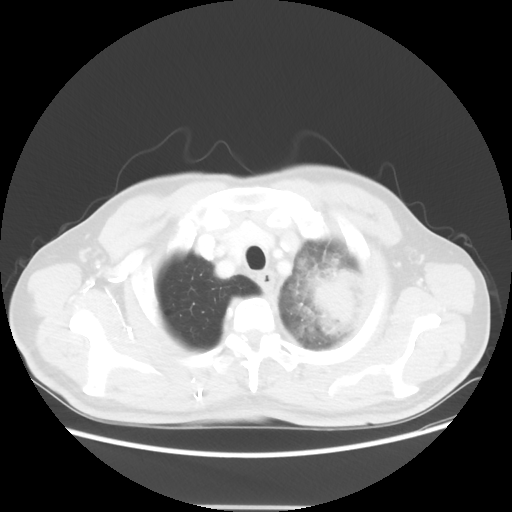
Chest CT, one axial slice. Slice 50 of 53 in the series (ordered by position). Reconstruction kernel STANDARD. 100 kVp. Lung window (W 1500 / L -600 HU). 5 mm slice thickness. 512 × 512 image matrix, field of view 391 × 391 mm. Patient: male, 60 years. Case-level facts recorded for this patient, not image findings: clinical TNM (as recorded): T4 N1 M1a; histopathological grade: G3.
Annotated regions visible in this slice (bounding box drawn by a radiologist):
- lung tumour (recorded histology: large cell carcinoma): bounding box [x1, y1, x2, y2] px = [304, 259, 371, 335]